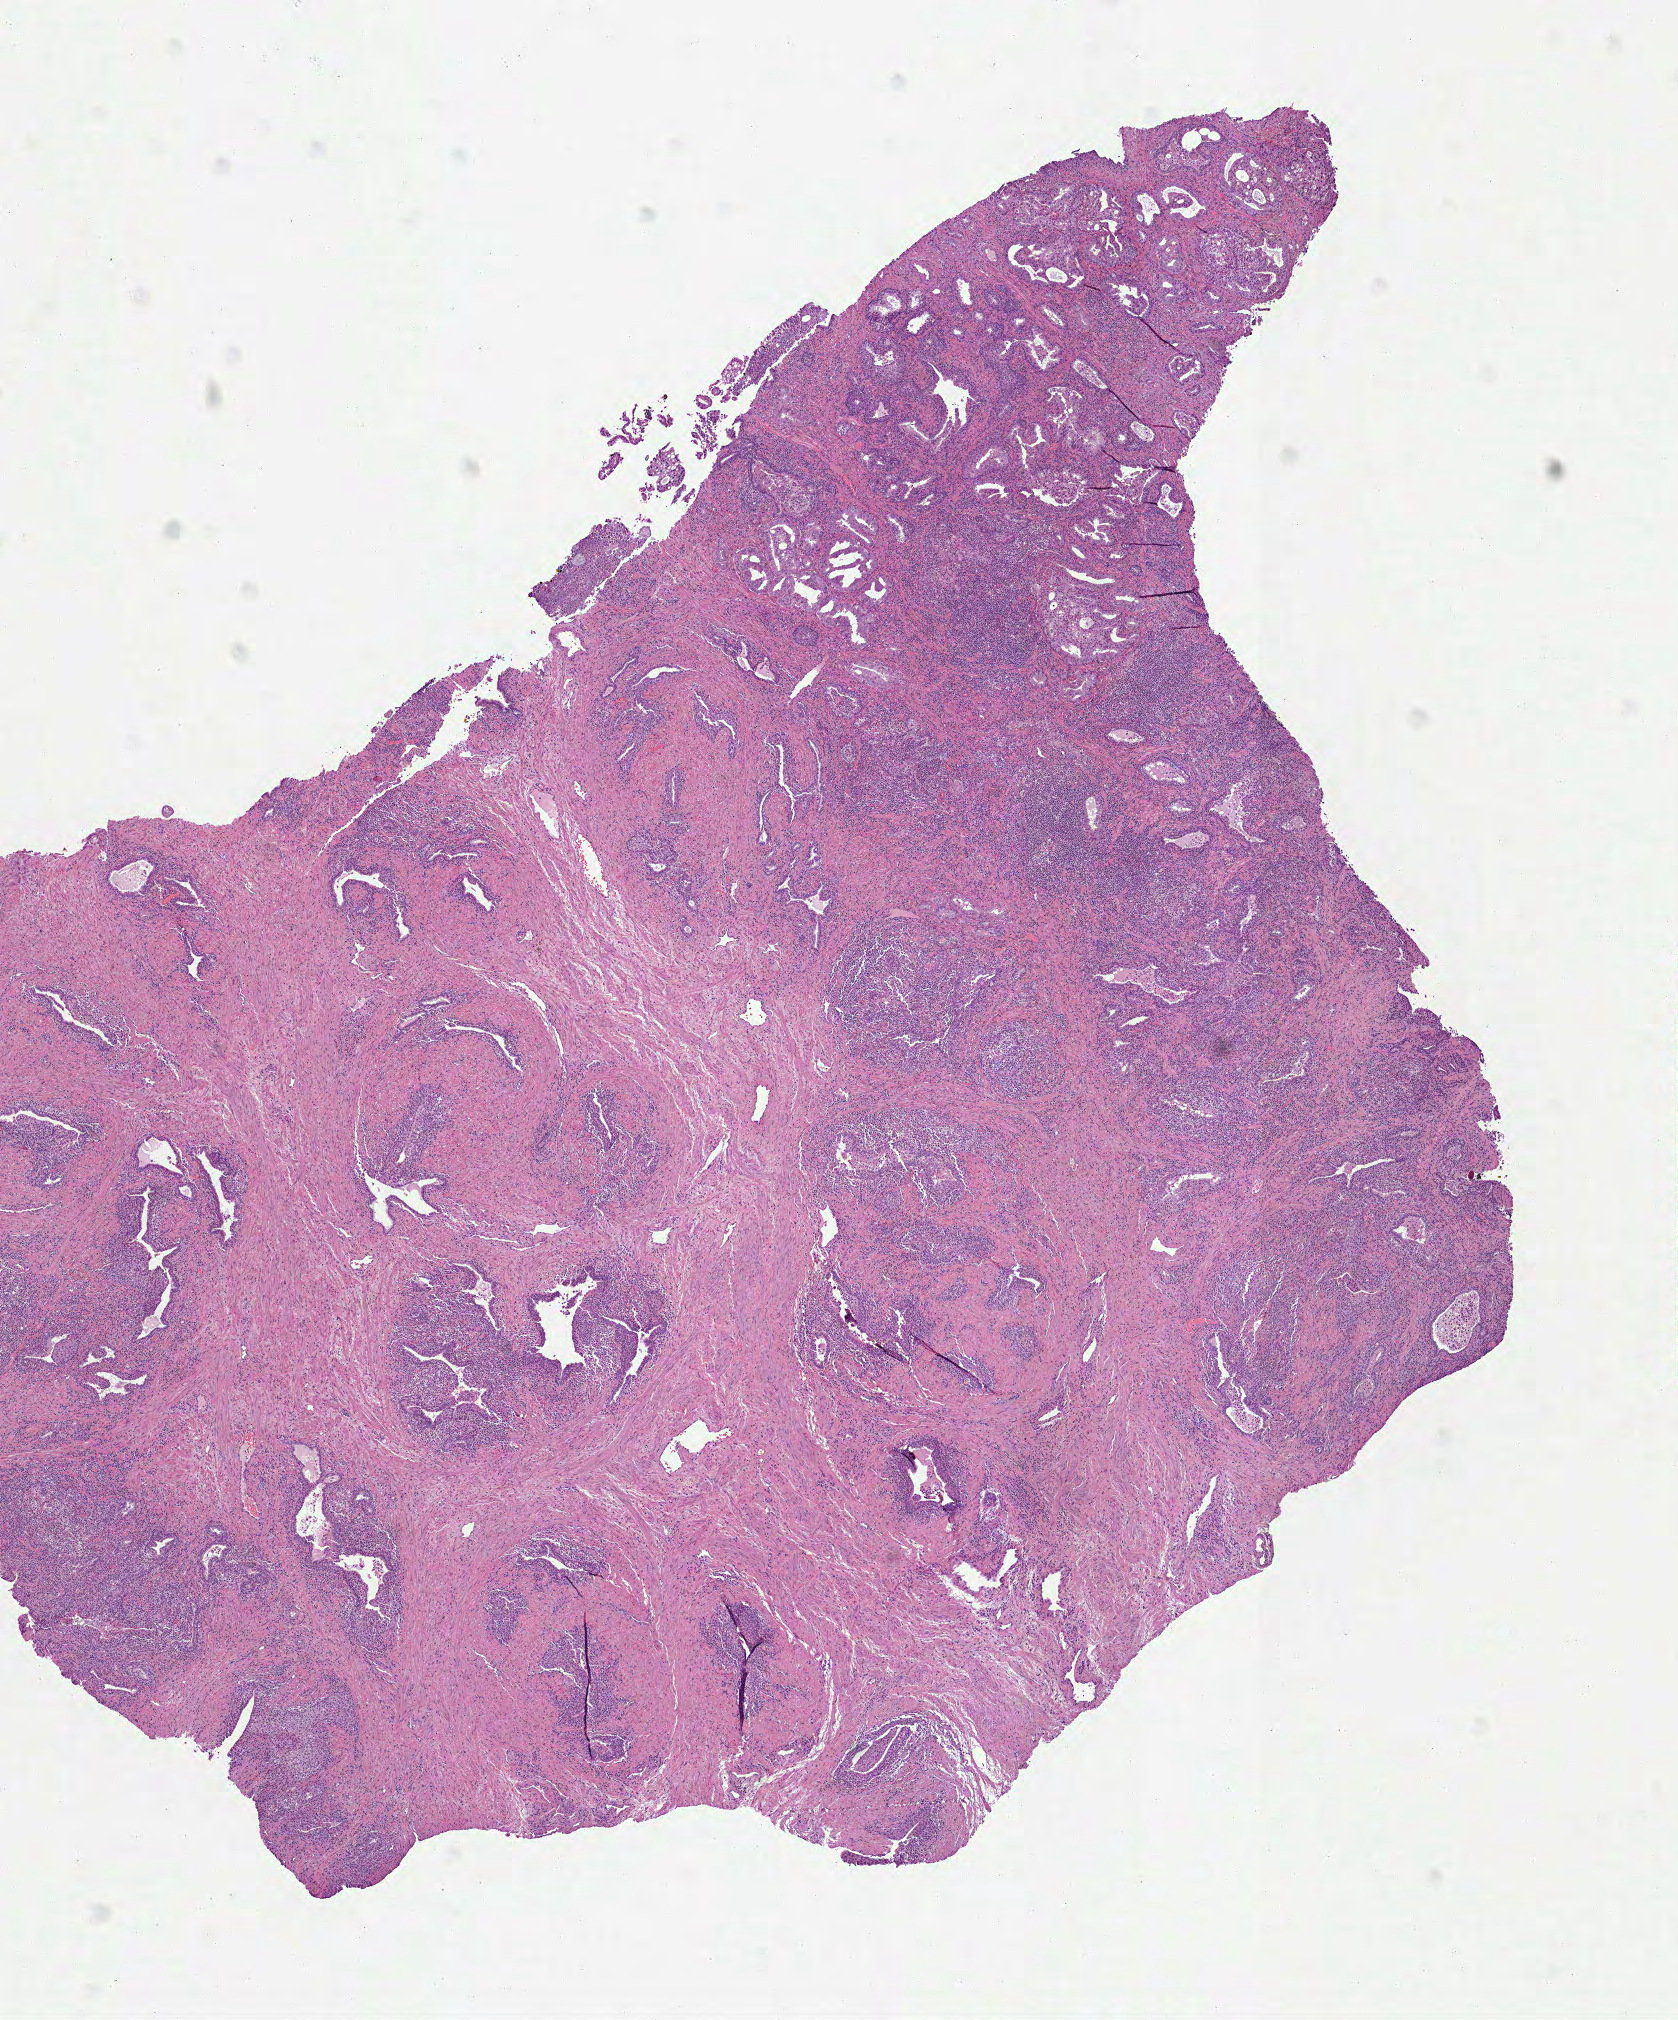
Whole-slide histology image, H&E, a low-resolution overview of the entire scanned area, about 6.8 x 8.1 mm. FFPE section. Primary tumour sample from the prostate. Male, age 51 years at initial diagnosis. Gleason score: 7 (3+4).
Laterality: bilateral. Pathologic diagnosis: Acinar cell carcinoma (prostate gland). Lymph nodes positive (case pathology): 0 of 4 examined.